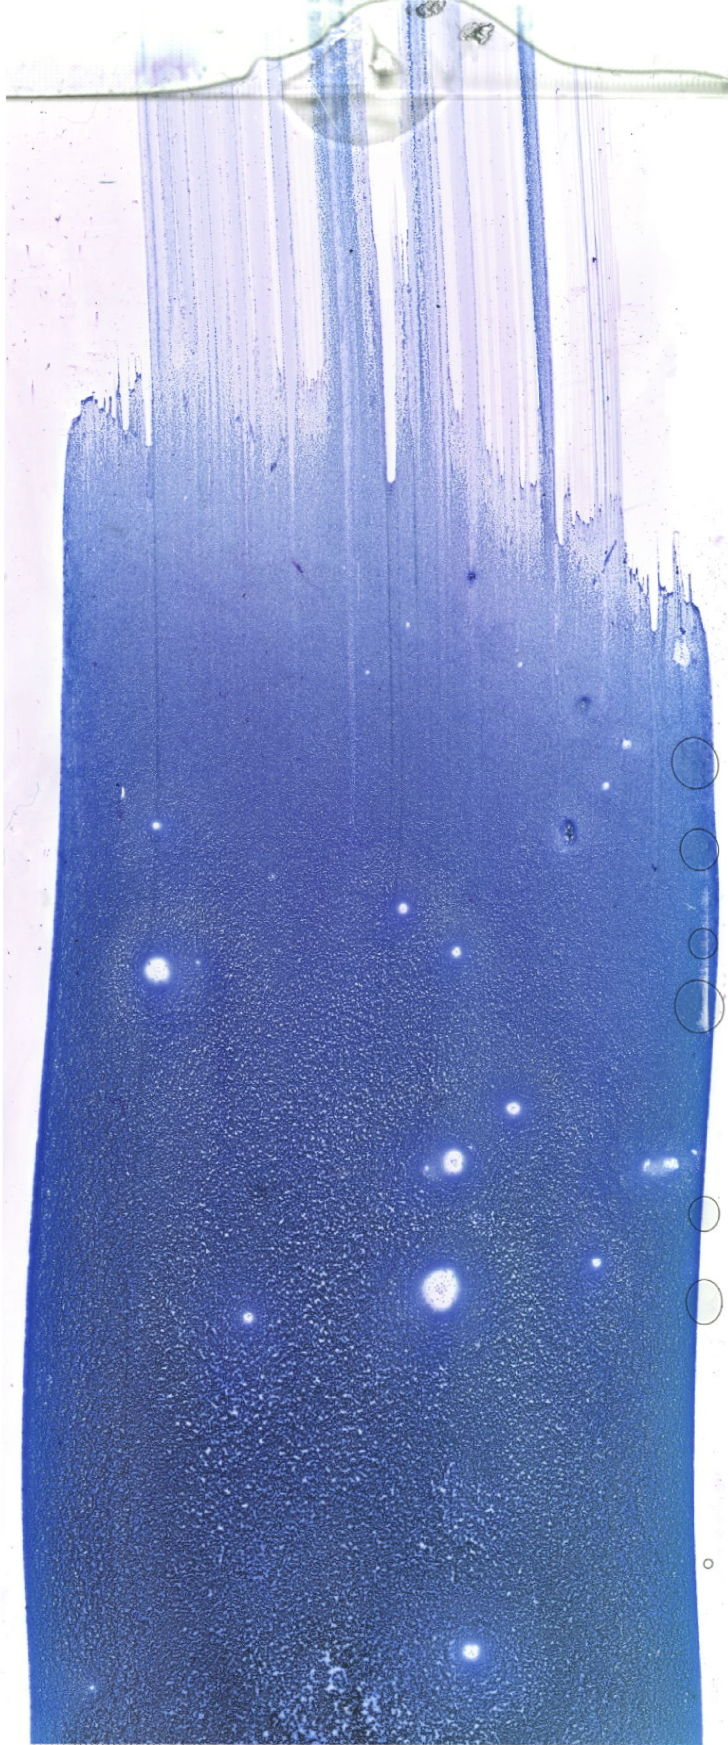
Whole-slide image of a May-Grünwald–Giemsa-stained bone marrow aspirate smear, whole scanned area (about 20.6 x 49.5 mm) shown as a low-resolution overview. Female patient.
Diagnosis: Acute Promyelocytic Leukemia with t(15;17)(q24.1;q21.2);PML-RARA.